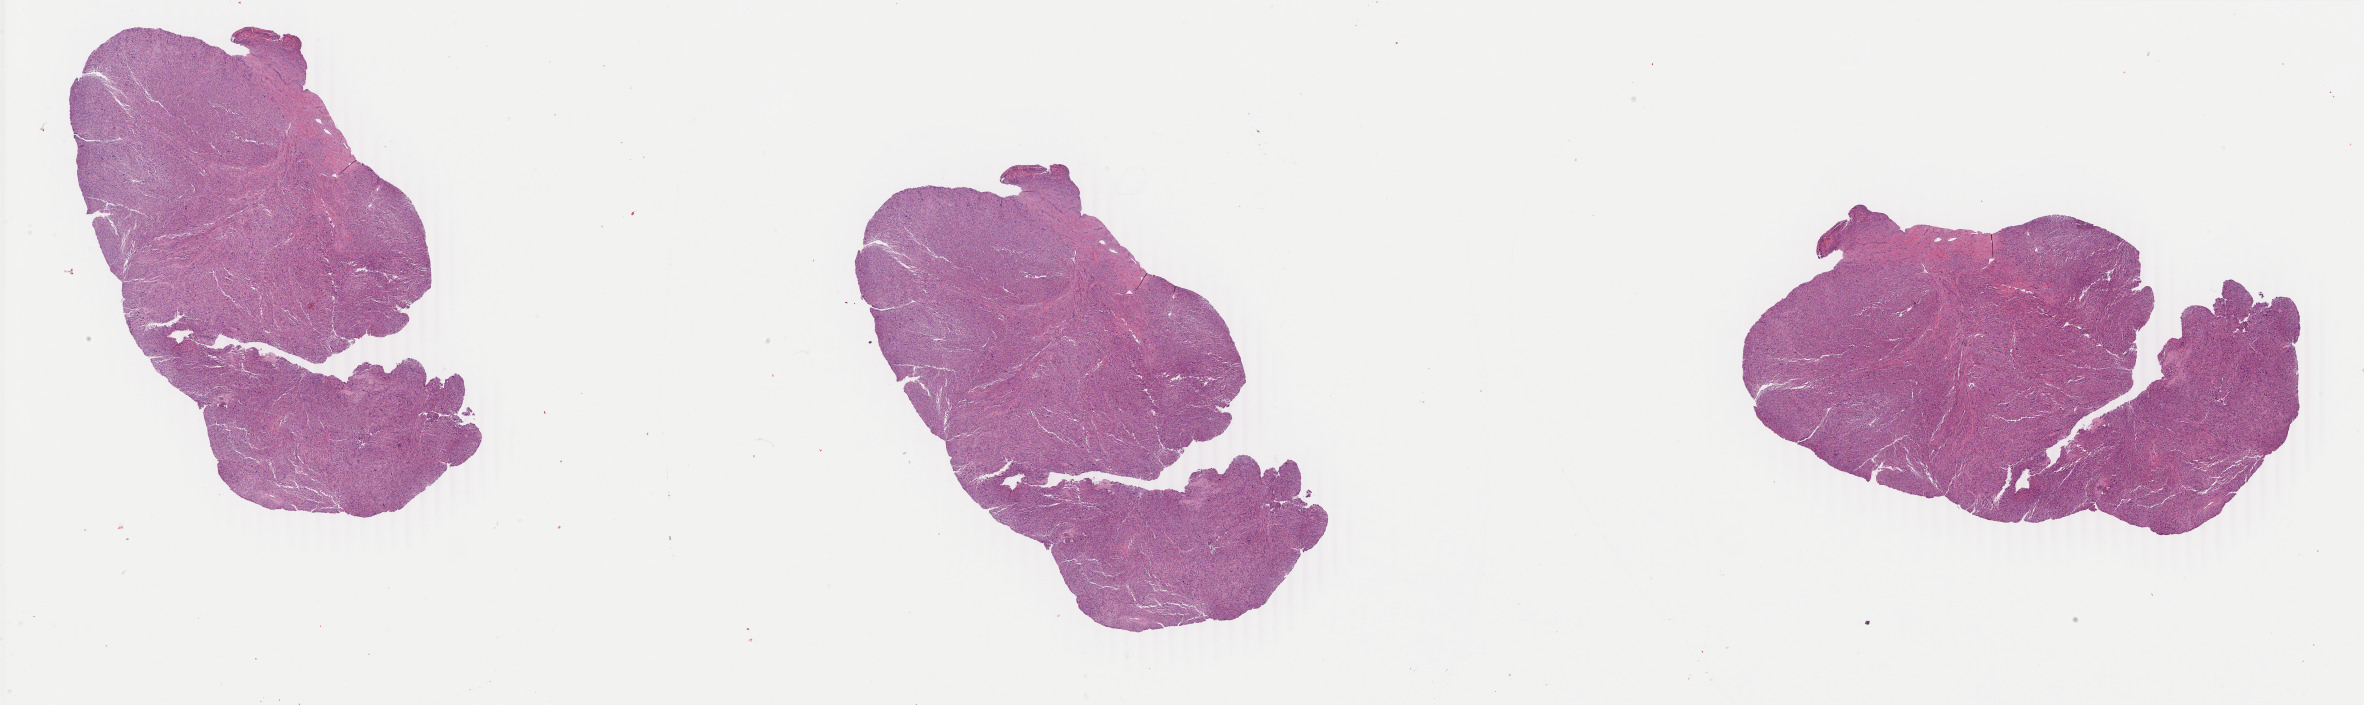
H&E whole-slide image — shown as a low-resolution overview of the whole scanned area (about 37.6 x 11.2 mm, from a 40x scan), FFPE section, corpus uteri, primary tumour sample. Patient: female, age at initial diagnosis 35 years.
Diagnosis: Leiomyosarcoma, NOS.